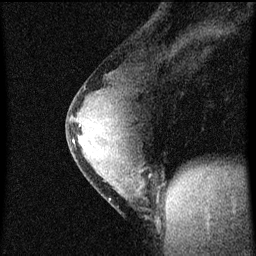
Breast MRI (dynamic contrast-enhanced), one sagittal slice; slice 32 of 60 in the series (ordered by position); dynamic contrast-enhanced series, image 2 of 4 at this slice position (ordered by acquisition); 1.5 T; TE 4.2 ms, TR 8 ms; 2 mm slice thickness; 256 × 256 image matrix, field of view 180 × 180 mm. Patient: female, 33 years.
Outlined on this slice (semi-automatic segmentation, software-assisted and operator-edited):
- analysis volume of interest (the breast-tissue region the enhancement analysis was run in; not a lesion): box from (x=67, y=76) to (x=157, y=217) px
- tumour enhancement mask (voxels above the 70 % enhancement threshold inside the analysis volume of interest): (x=73, y=126)–(x=140, y=173)